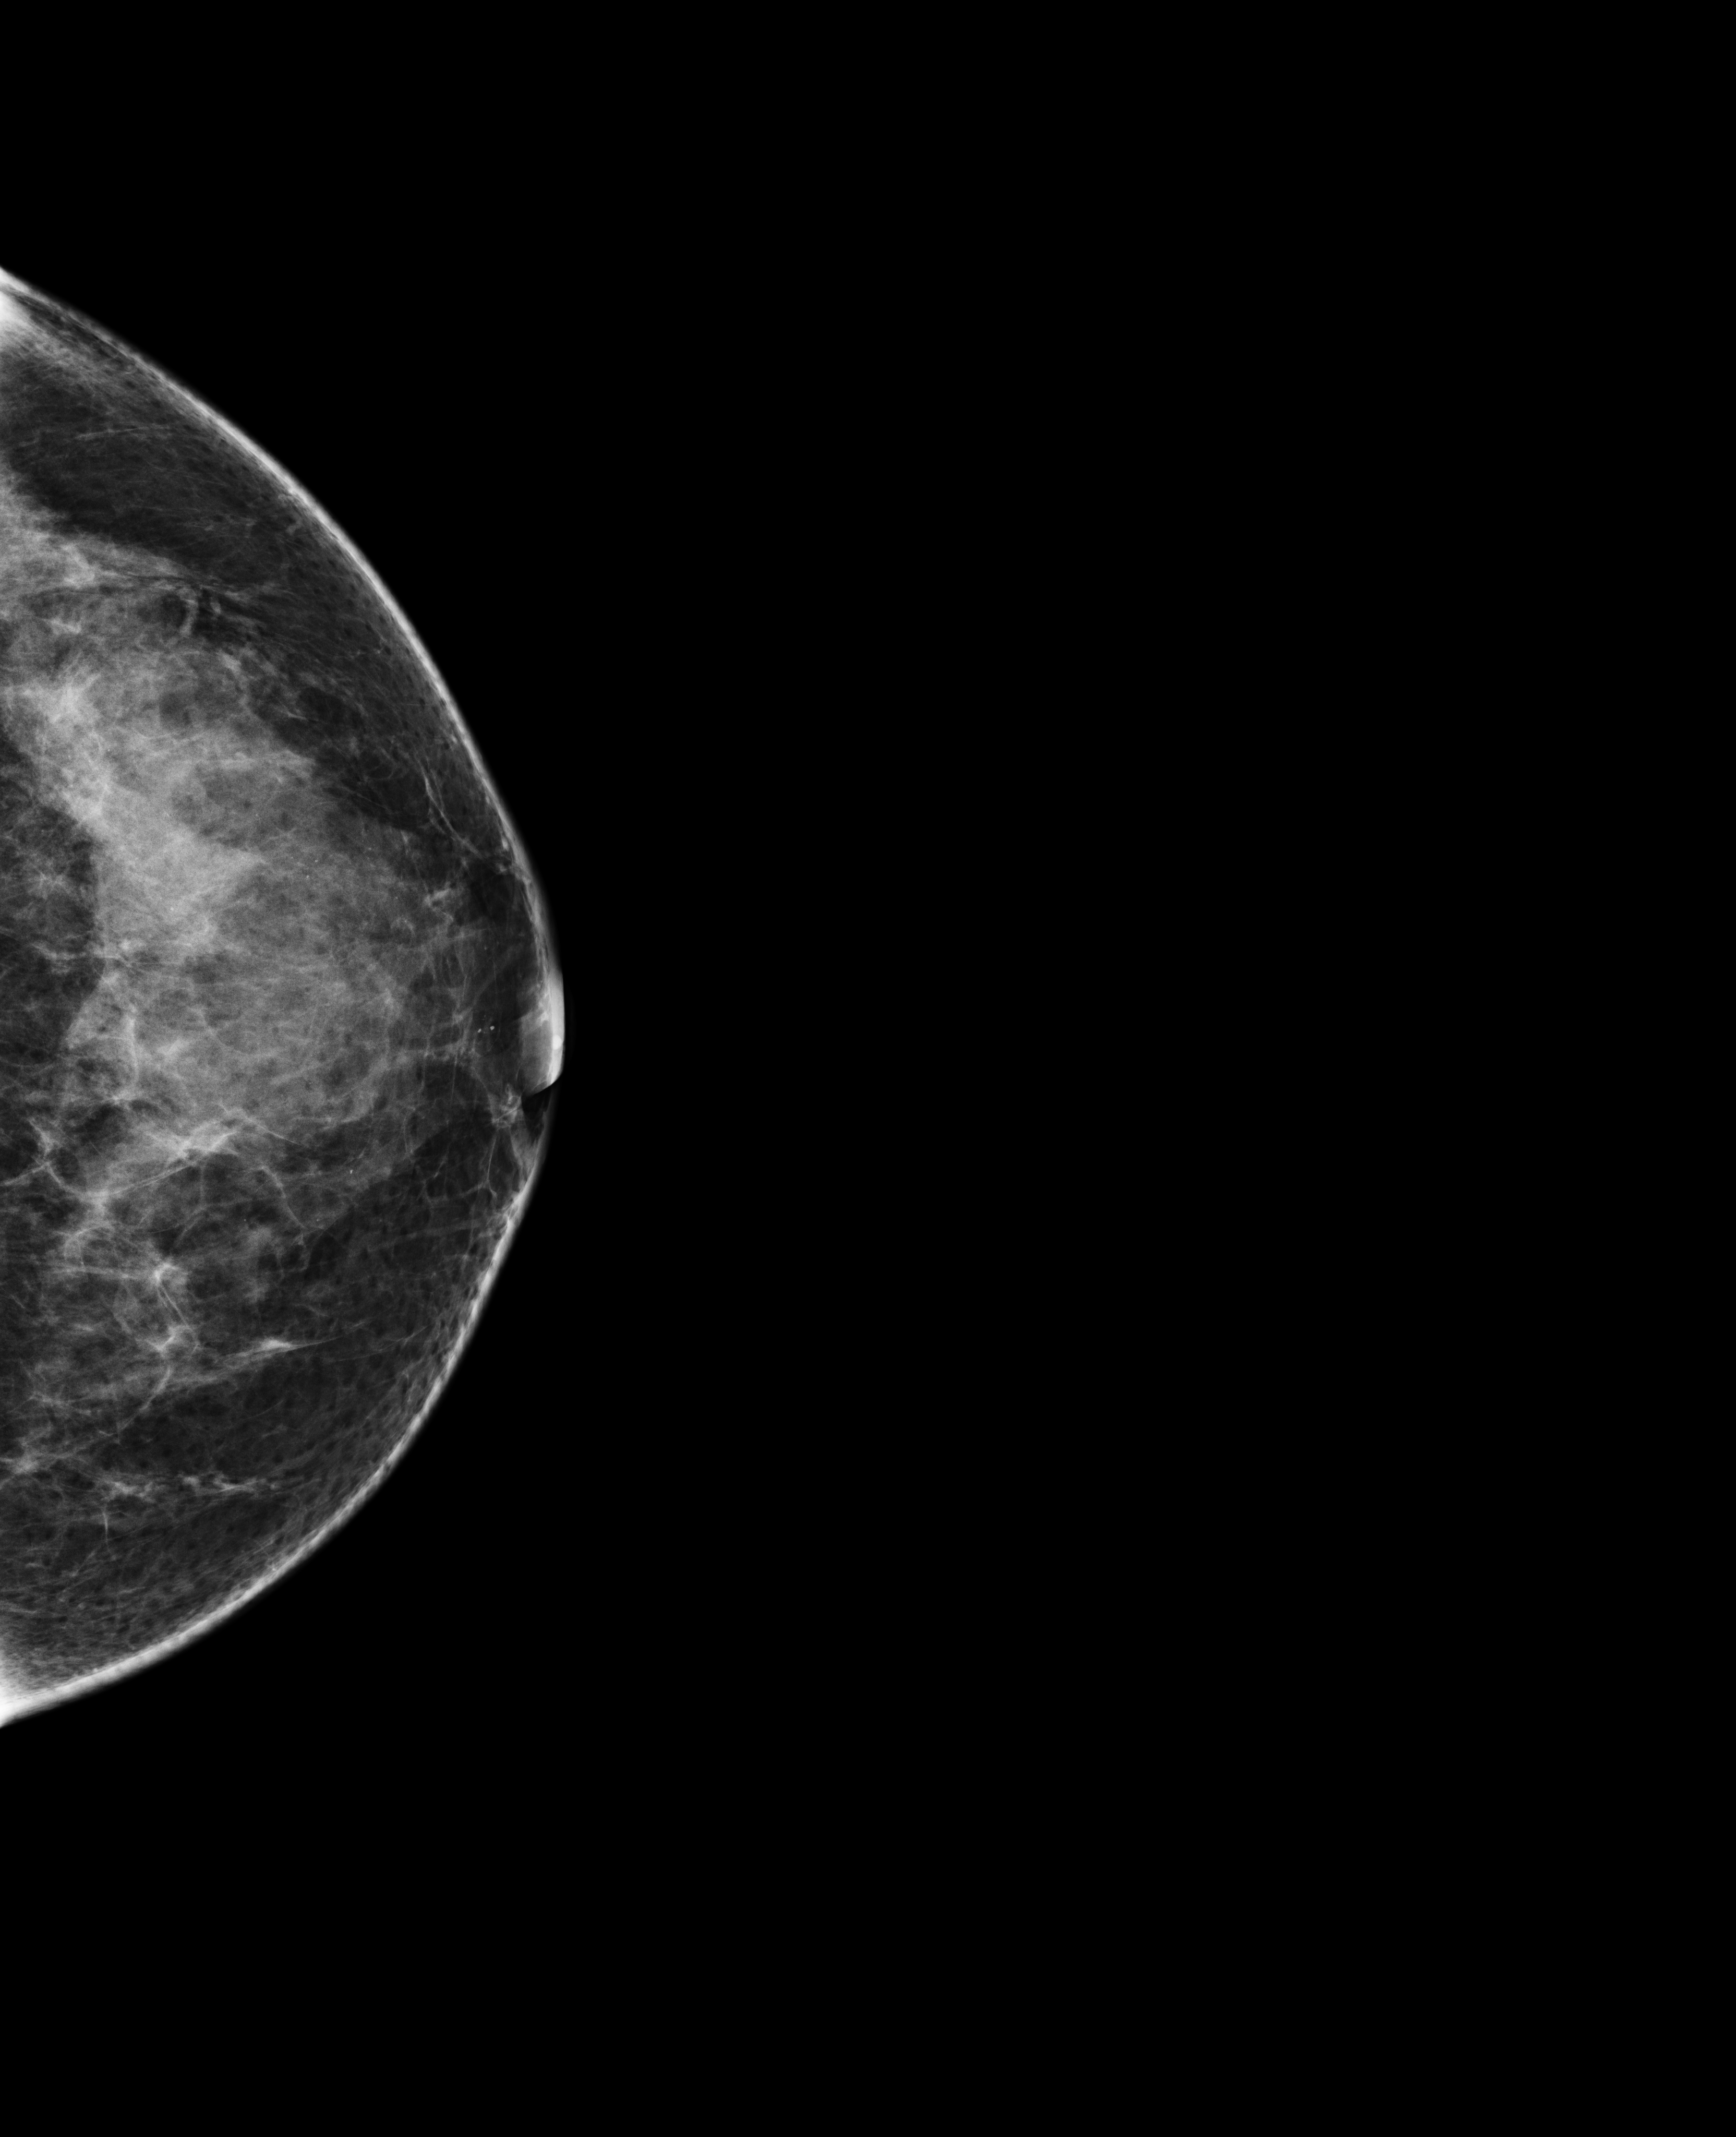
Full-field digital mammogram (FFDM), left breast, cranio-caudal projection, annual screening mammography examination, system: Selenia Dimensions. Female patient, age 48 years.
Breast density at the screening exam (both breasts): heterogeneously dense (BI-RADS density category c). Final BI-RADS assessment for this screening round (tomosynthesis exam, both breasts): category 4. Recall: recalled for additional imaging after this screen.